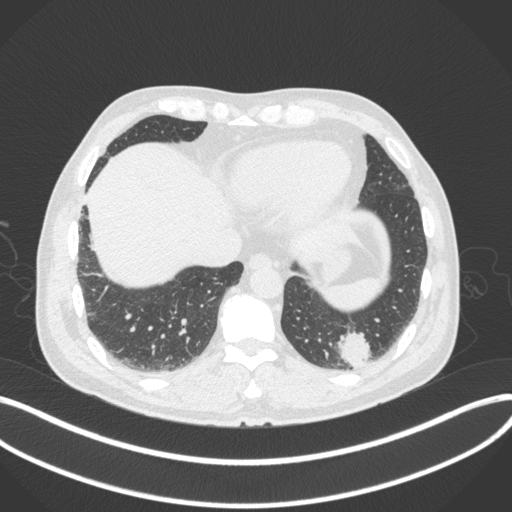
Chest CT, one axial slice; position 62 of 313 along the scan axis; reconstruction kernel B31f; 120 kVp; lung window (W 1500 / L -600 HU); 1 mm slice thickness; 512 × 512 image matrix. Male patient, age 54 years. From the clinical record (not read from this slice): clinical TNM (as recorded): T1c N0 M1; histopathological grade: G3.
Outlined on this slice (bounding box drawn by a radiologist):
- lung tumour (recorded histology: adenocarcinoma): box from (x=335, y=326) to (x=373, y=369) px